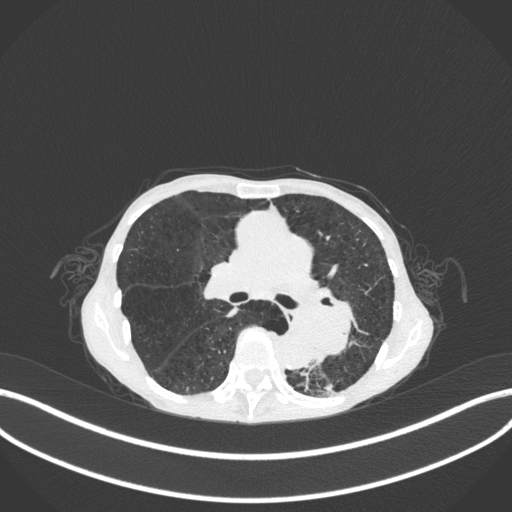
Chest CT, one axial slice; position 164 of 347 along the scan axis; reconstruction kernel B31f; 120 kVp; lung window (W 1500 / L -600 HU); 1 mm slice thickness; 512 × 512 image matrix. Female patient, age 70 years. Case-level facts recorded for this patient, not image findings: clinical TNM (as recorded): T3 N0 M0; histopathological grade: G3.
Structures marked on this image (rectangle marked by the reading radiologist):
- lung tumour (recorded histology: small cell carcinoma): bounding box (x1, y1, x2, y2) in pixels: (303, 280, 360, 364)